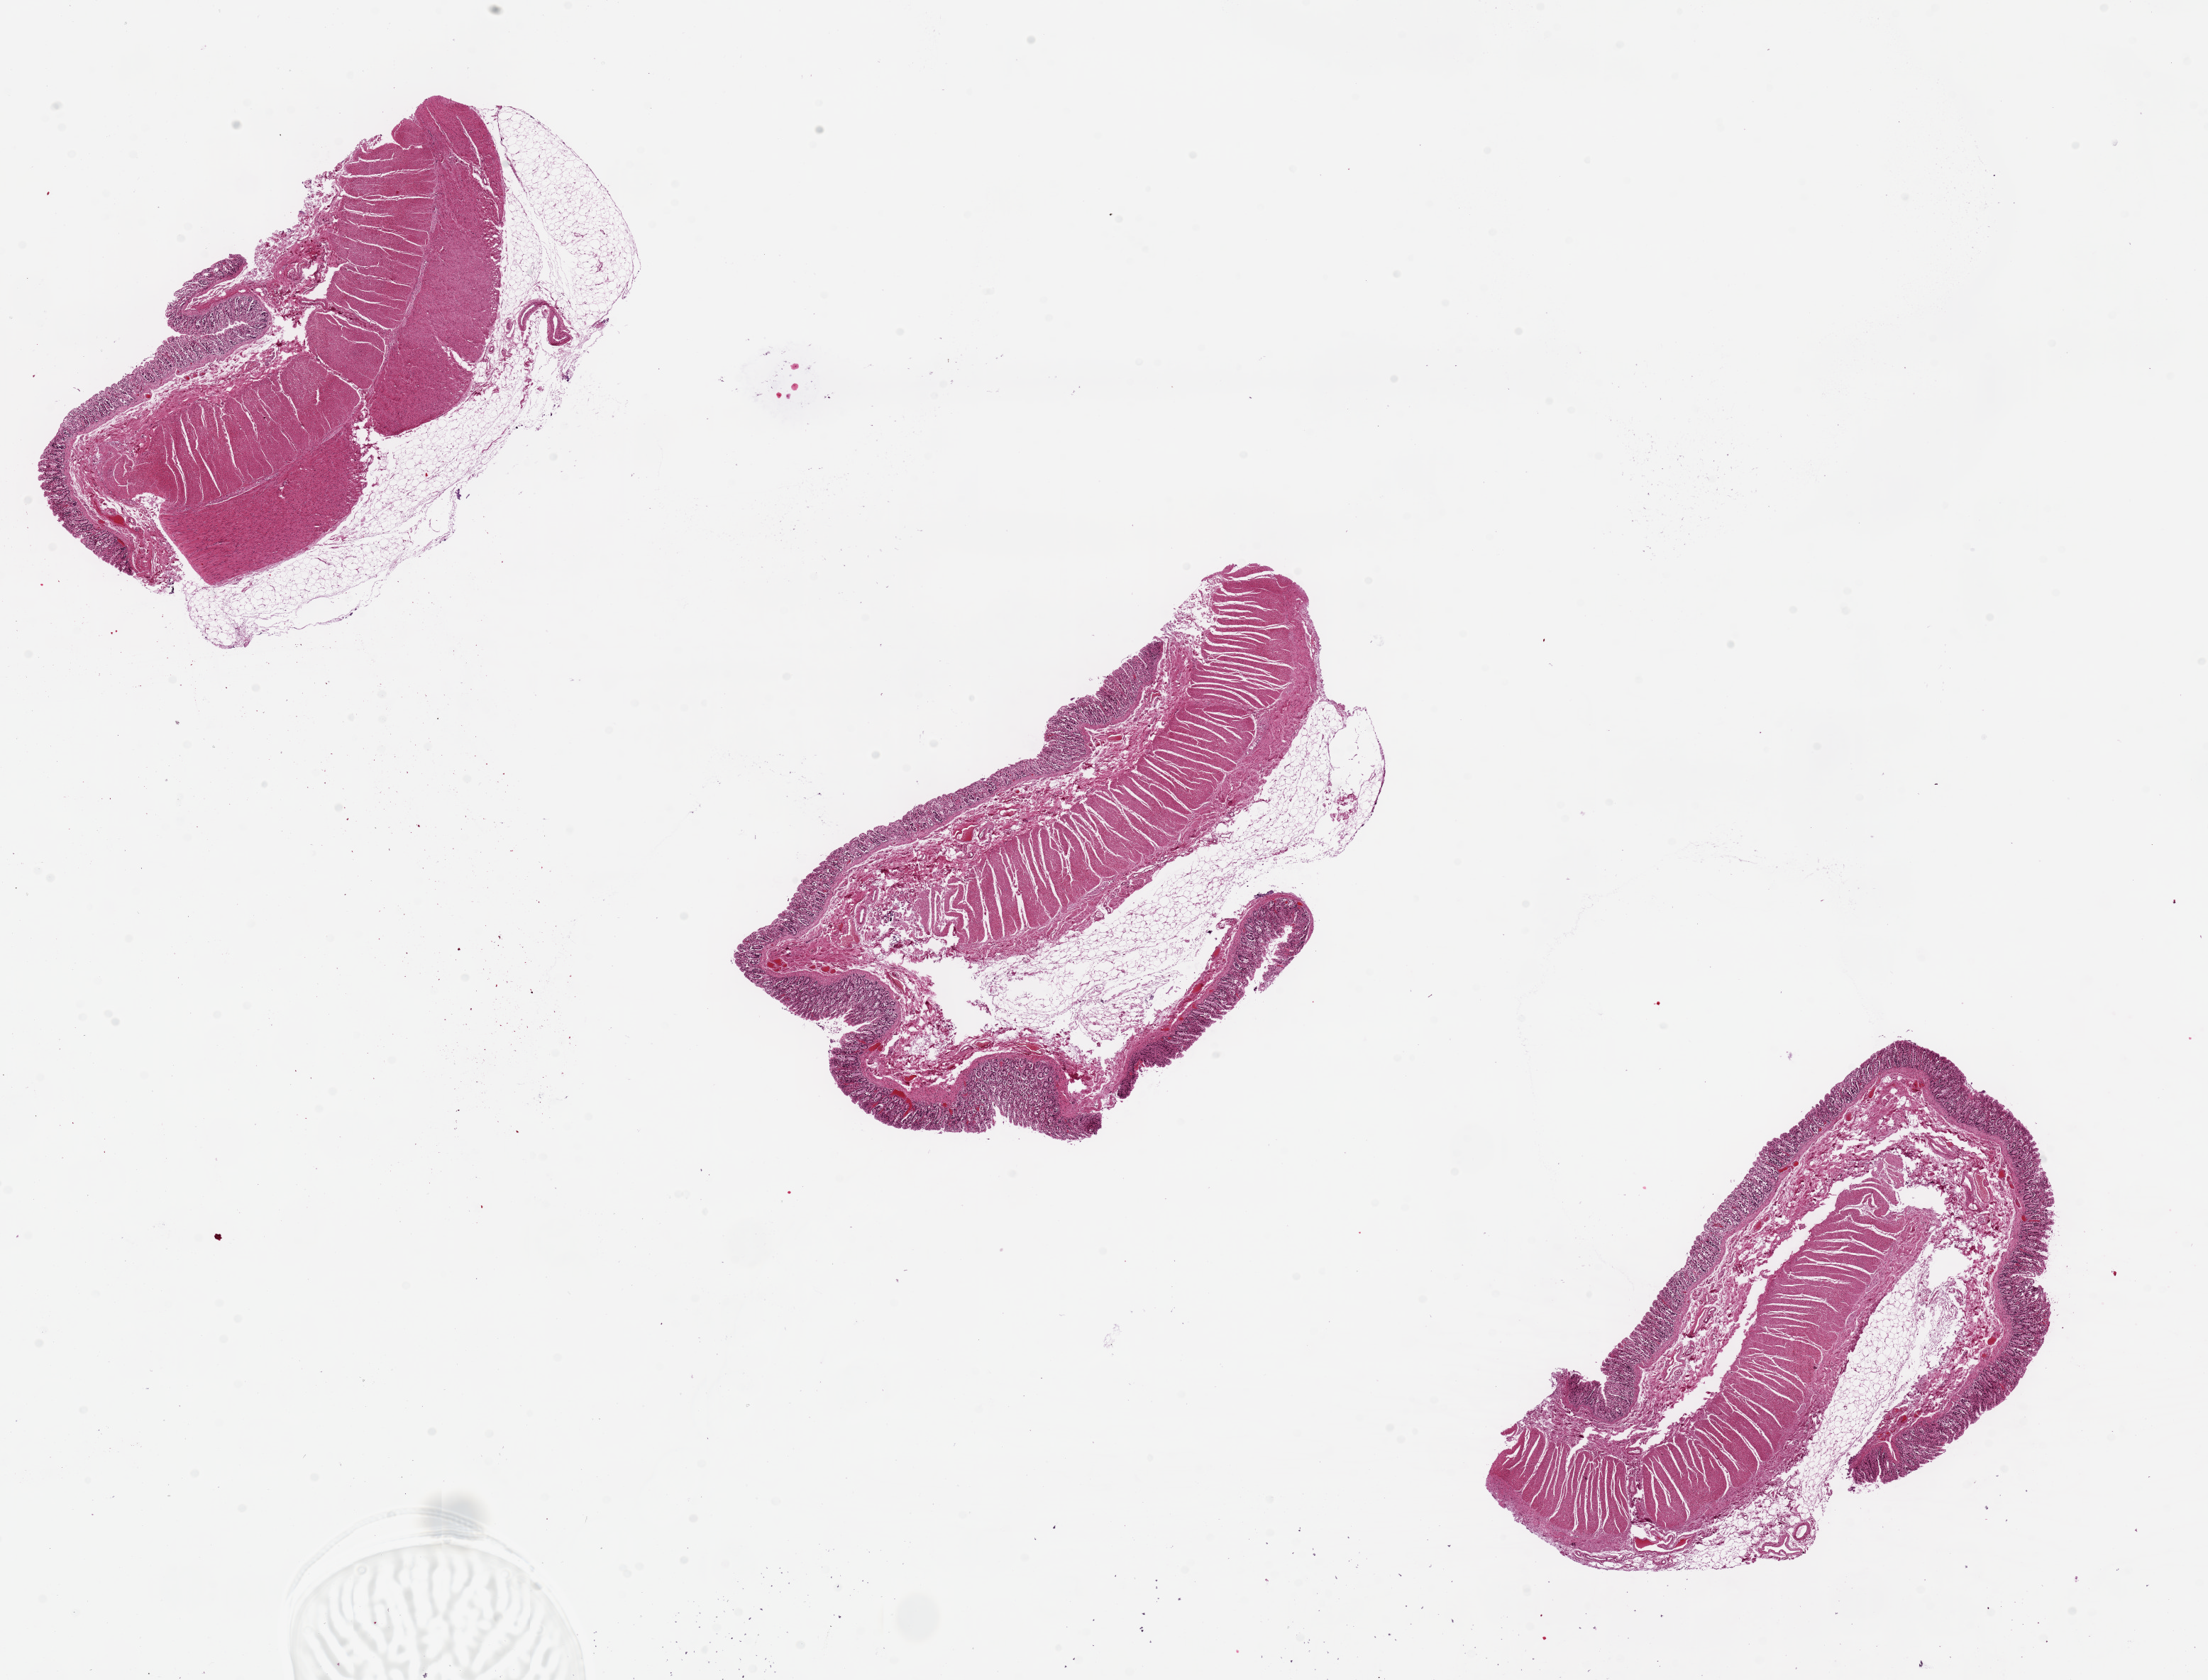
Hematoxylin and eosin (H&E) whole-slide image, low-resolution overview of the scanned area, about 24.6 x 18.7 mm (acquisition: 20x scan). PAXgene-fixed, paraffin-embedded tissue. Section of transverse colon (target tissue). Donor tissue sample. Donor sex: female.
Review note (as recorded): Epithelial autolysis ~100% (???score 3???).